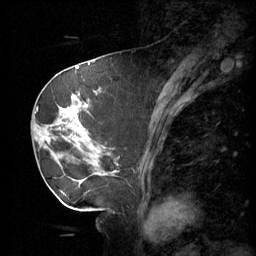
Breast MRI (dynamic contrast-enhanced), one sagittal slice. Slice 24 of 60 in the series (ordered by position). 3 images stored at this slice position (order not interpretable as contrast timing). 1.5 T. TE 4.2 ms, TR 11 ms. 2 mm slice thickness. 256 × 256 image matrix, field of view 220 × 220 mm. Patient: female, 69 years.
Annotated regions visible in this slice (semi-automatic segmentation, software-assisted and operator-edited):
- analysis volume of interest (the breast-tissue region the enhancement analysis was run in; not a lesion): bounding box [x1, y1, x2, y2] px = [36, 88, 116, 189]
- tumour enhancement mask (voxels above the 70 % enhancement threshold inside the analysis volume of interest): [57, 96, 105, 181]